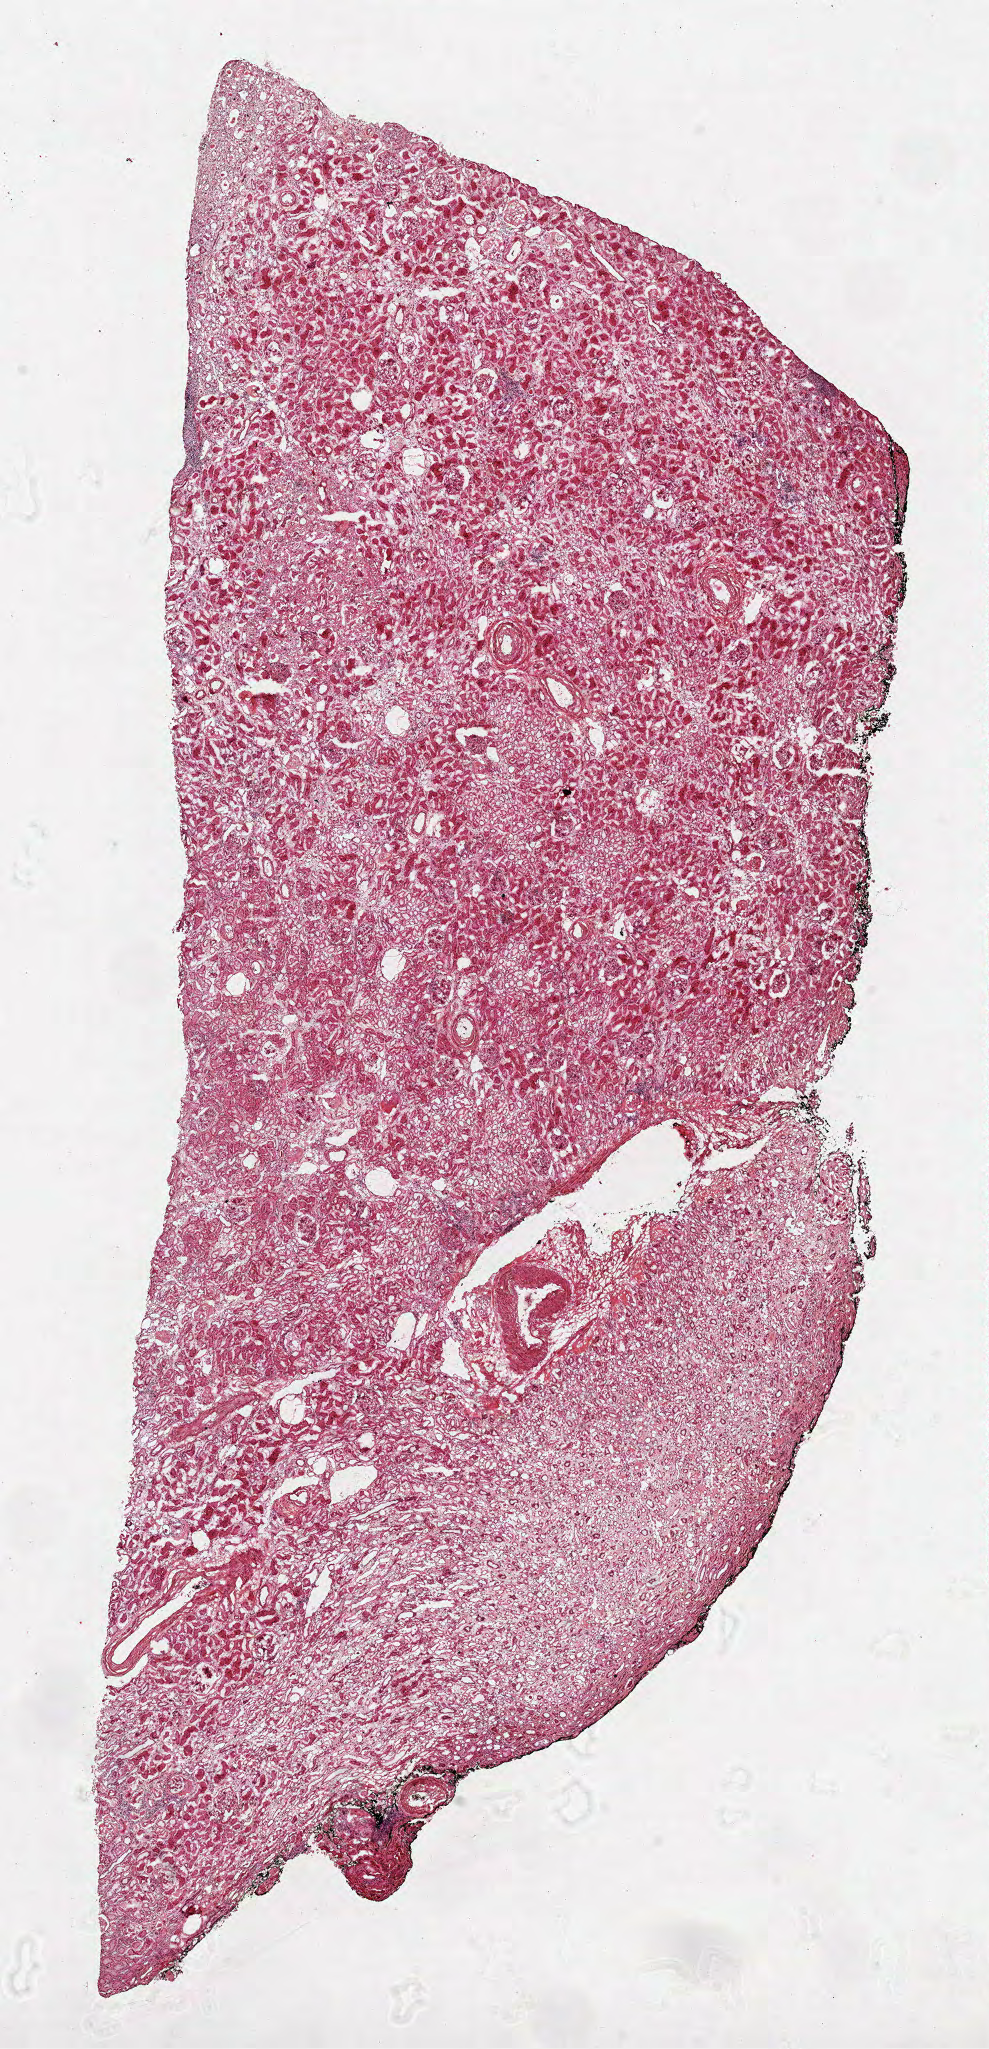
Whole-slide histology image, H&E, whole scanned area (about 8.0 x 16.5 mm, acquisition: 40x scan) shown as a low-resolution overview. Frozen section from the top of the tissue portion. Solid tissue normal (non-tumour tissue) sample from the kidney. Male, age 64 years at initial diagnosis.
This section: solid tissue normal sample (biorepository sample class). Patient diagnosis: Papillary adenocarcinoma, NOS.